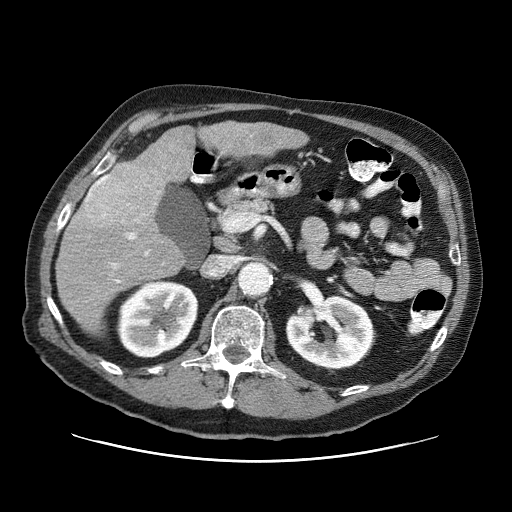
Contrast-enhanced abdominal CT (liver protocol), one axial slice. Position 32 of 87 along the scan axis. Reconstruction kernel STANDARD. One of 3 acquisitions stored at this slice position. Soft-tissue window (W 400 / L 40 HU). 2.5 mm slice thickness. 512 × 512 image matrix, field of view 400 × 400 mm. From the clinical record (not read from this slice): diagnosis: hepatocellular carcinoma (patient treated with transarterial chemoembolisation; whether this scan precedes or follows treatment is not stated here); TNM stage (as recorded): Stage-IIIA; Child-Pugh class: A; tumour differentiation: well differentiated; tumour nodularity: multinodular.
Structures marked on this image (semi-automatically segmented with operator editing):
- liver parenchyma outside the tumour (the mass and vessels are separate outlines, so this box may not span the whole liver): bounding box (x1, y1, x2, y2) in pixels: (56, 122, 308, 334)
- mass: (68, 152, 164, 228)
- liver vessels: (113, 233, 149, 283)